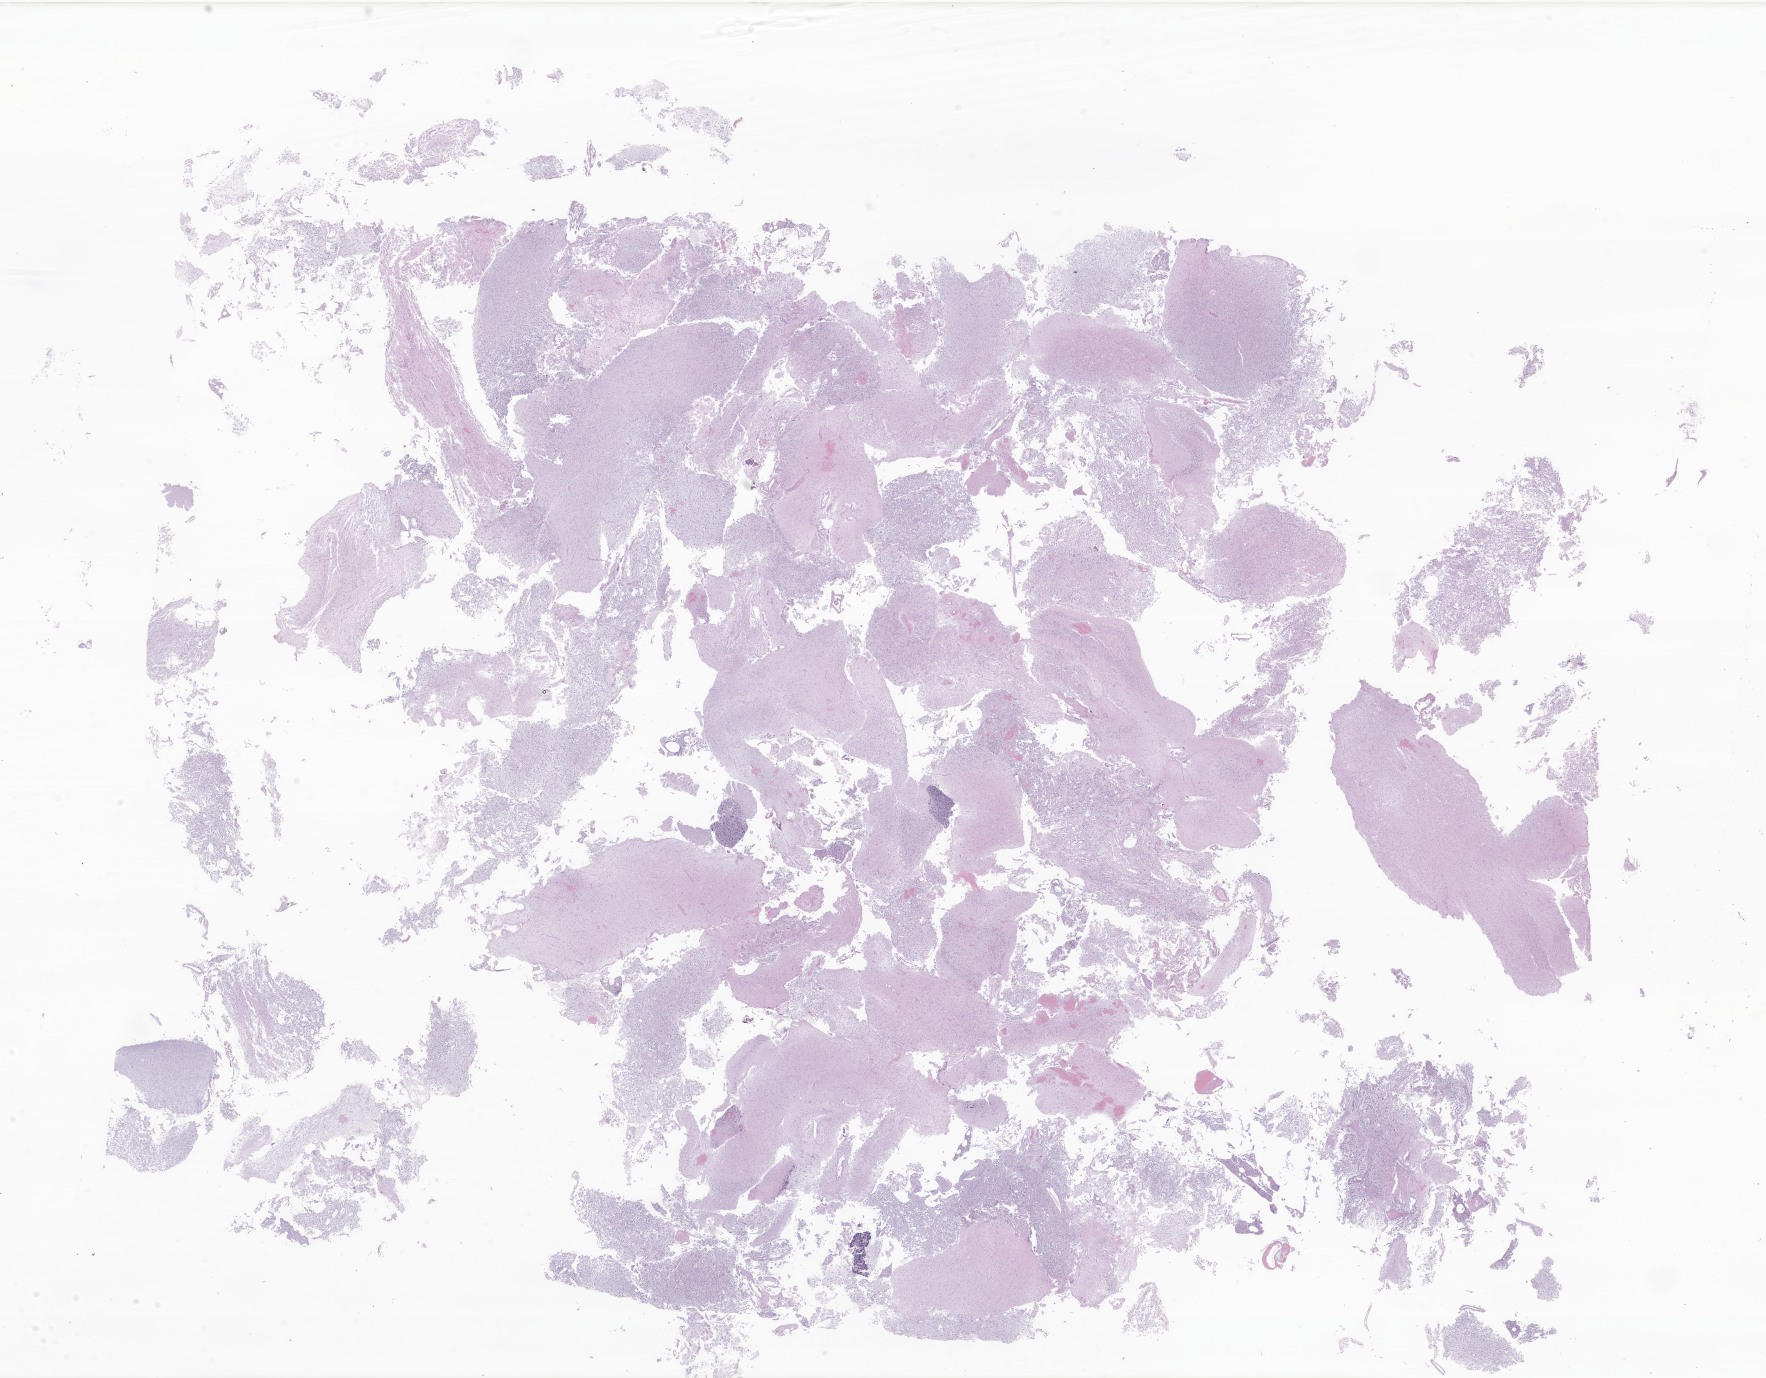
Whole-slide image, haematoxylin and eosin stain of tumor tissue from the brain, whole scanned area (about 29.8 x 23.2 mm) shown as a low-resolution overview. Formalin-fixed, paraffin-embedded (FFPE) tissue. Male patient, age 218 months (18 years 2 months).
Diagnosis: Neoplasm, malignant.